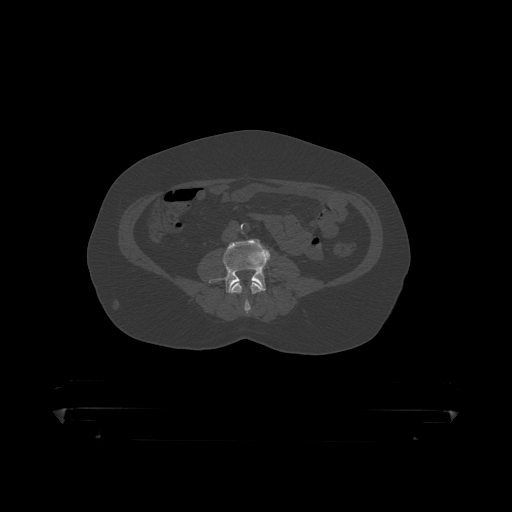
CT including the spine, one axial slice; position 74 of 390 along the scan axis; reconstruction kernel STANDARD; bone window (W 1800 / L 400 HU); 1.25 mm slice thickness; 512 × 512 image matrix, field of view 650 × 650 mm. Male patient, age 60 years. From the clinical record (not read from this slice): primary cancer: prostate.
Structures marked on this image (semi-automatic segmentation, software-assisted and operator-edited):
- L3 vertebra: bounding box [x1, y1, x2, y2] px = [230, 282, 263, 315]
- L4 vertebra: [209, 239, 270, 294]